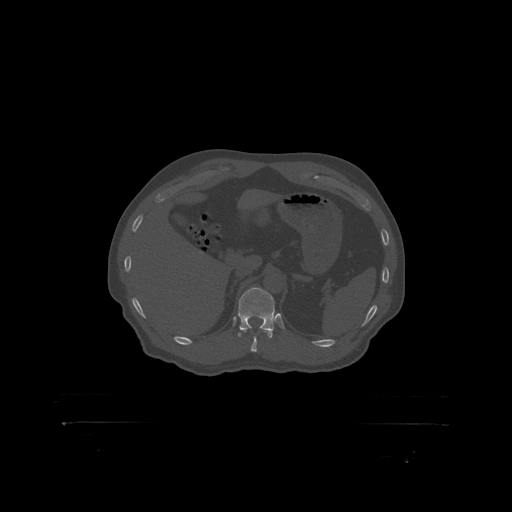
CT including the spine, one axial slice; slice 363 of 399 in the series (ordered by position); reconstruction kernel STANDARD; bone window (W 1800 / L 400 HU); 512 × 512 image matrix. Male patient, age 46 years. From the clinical record (not read from this slice): primary cancer: skin.
Outlined on this slice (semi-automatic segmentation, software-assisted and operator-edited):
- T12 vertebra: bounding box [x1, y1, x2, y2] px = [238, 288, 280, 319]